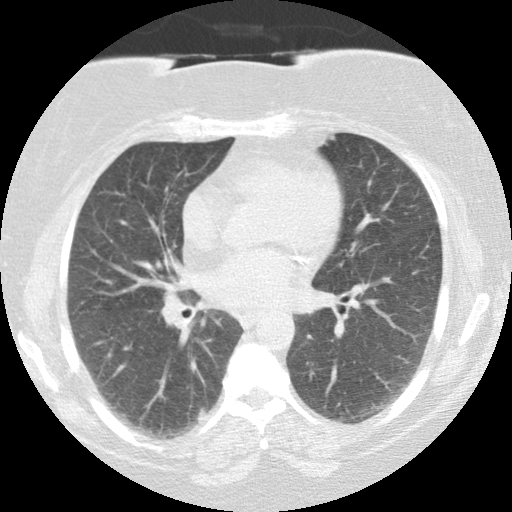
Chest CT (low-dose screening protocol), one axial image; baseline annual screen; lung window (W 1500 / L -600 HU); slice 54 of 111 in the series; 512 × 512 image matrix, field of view 316 × 316 mm. Female participant, aged 58 years at enrolment. Current smoker at enrolment.
Expert-annotated lung lesion, bounding box [x1, y1, x2, y2] px = [174, 393, 225, 444]. The screening reader recorded 4 non-calcified nodules or masses ≥4 mm on this exam; which of them this box marks is not recorded. Official screen result: positive, change unspecified: nodule(s) >= 4 mm or enlarging nodule(s), mass(es), or other non-specific abnormalities suspicious for lung cancer. Later outcome: lung cancer diagnosed 644 days after this screen — adenocarcinoma, NOS, right lower lobe, stage IIIA (AJCC 6th edition), 25 mm at pathology.